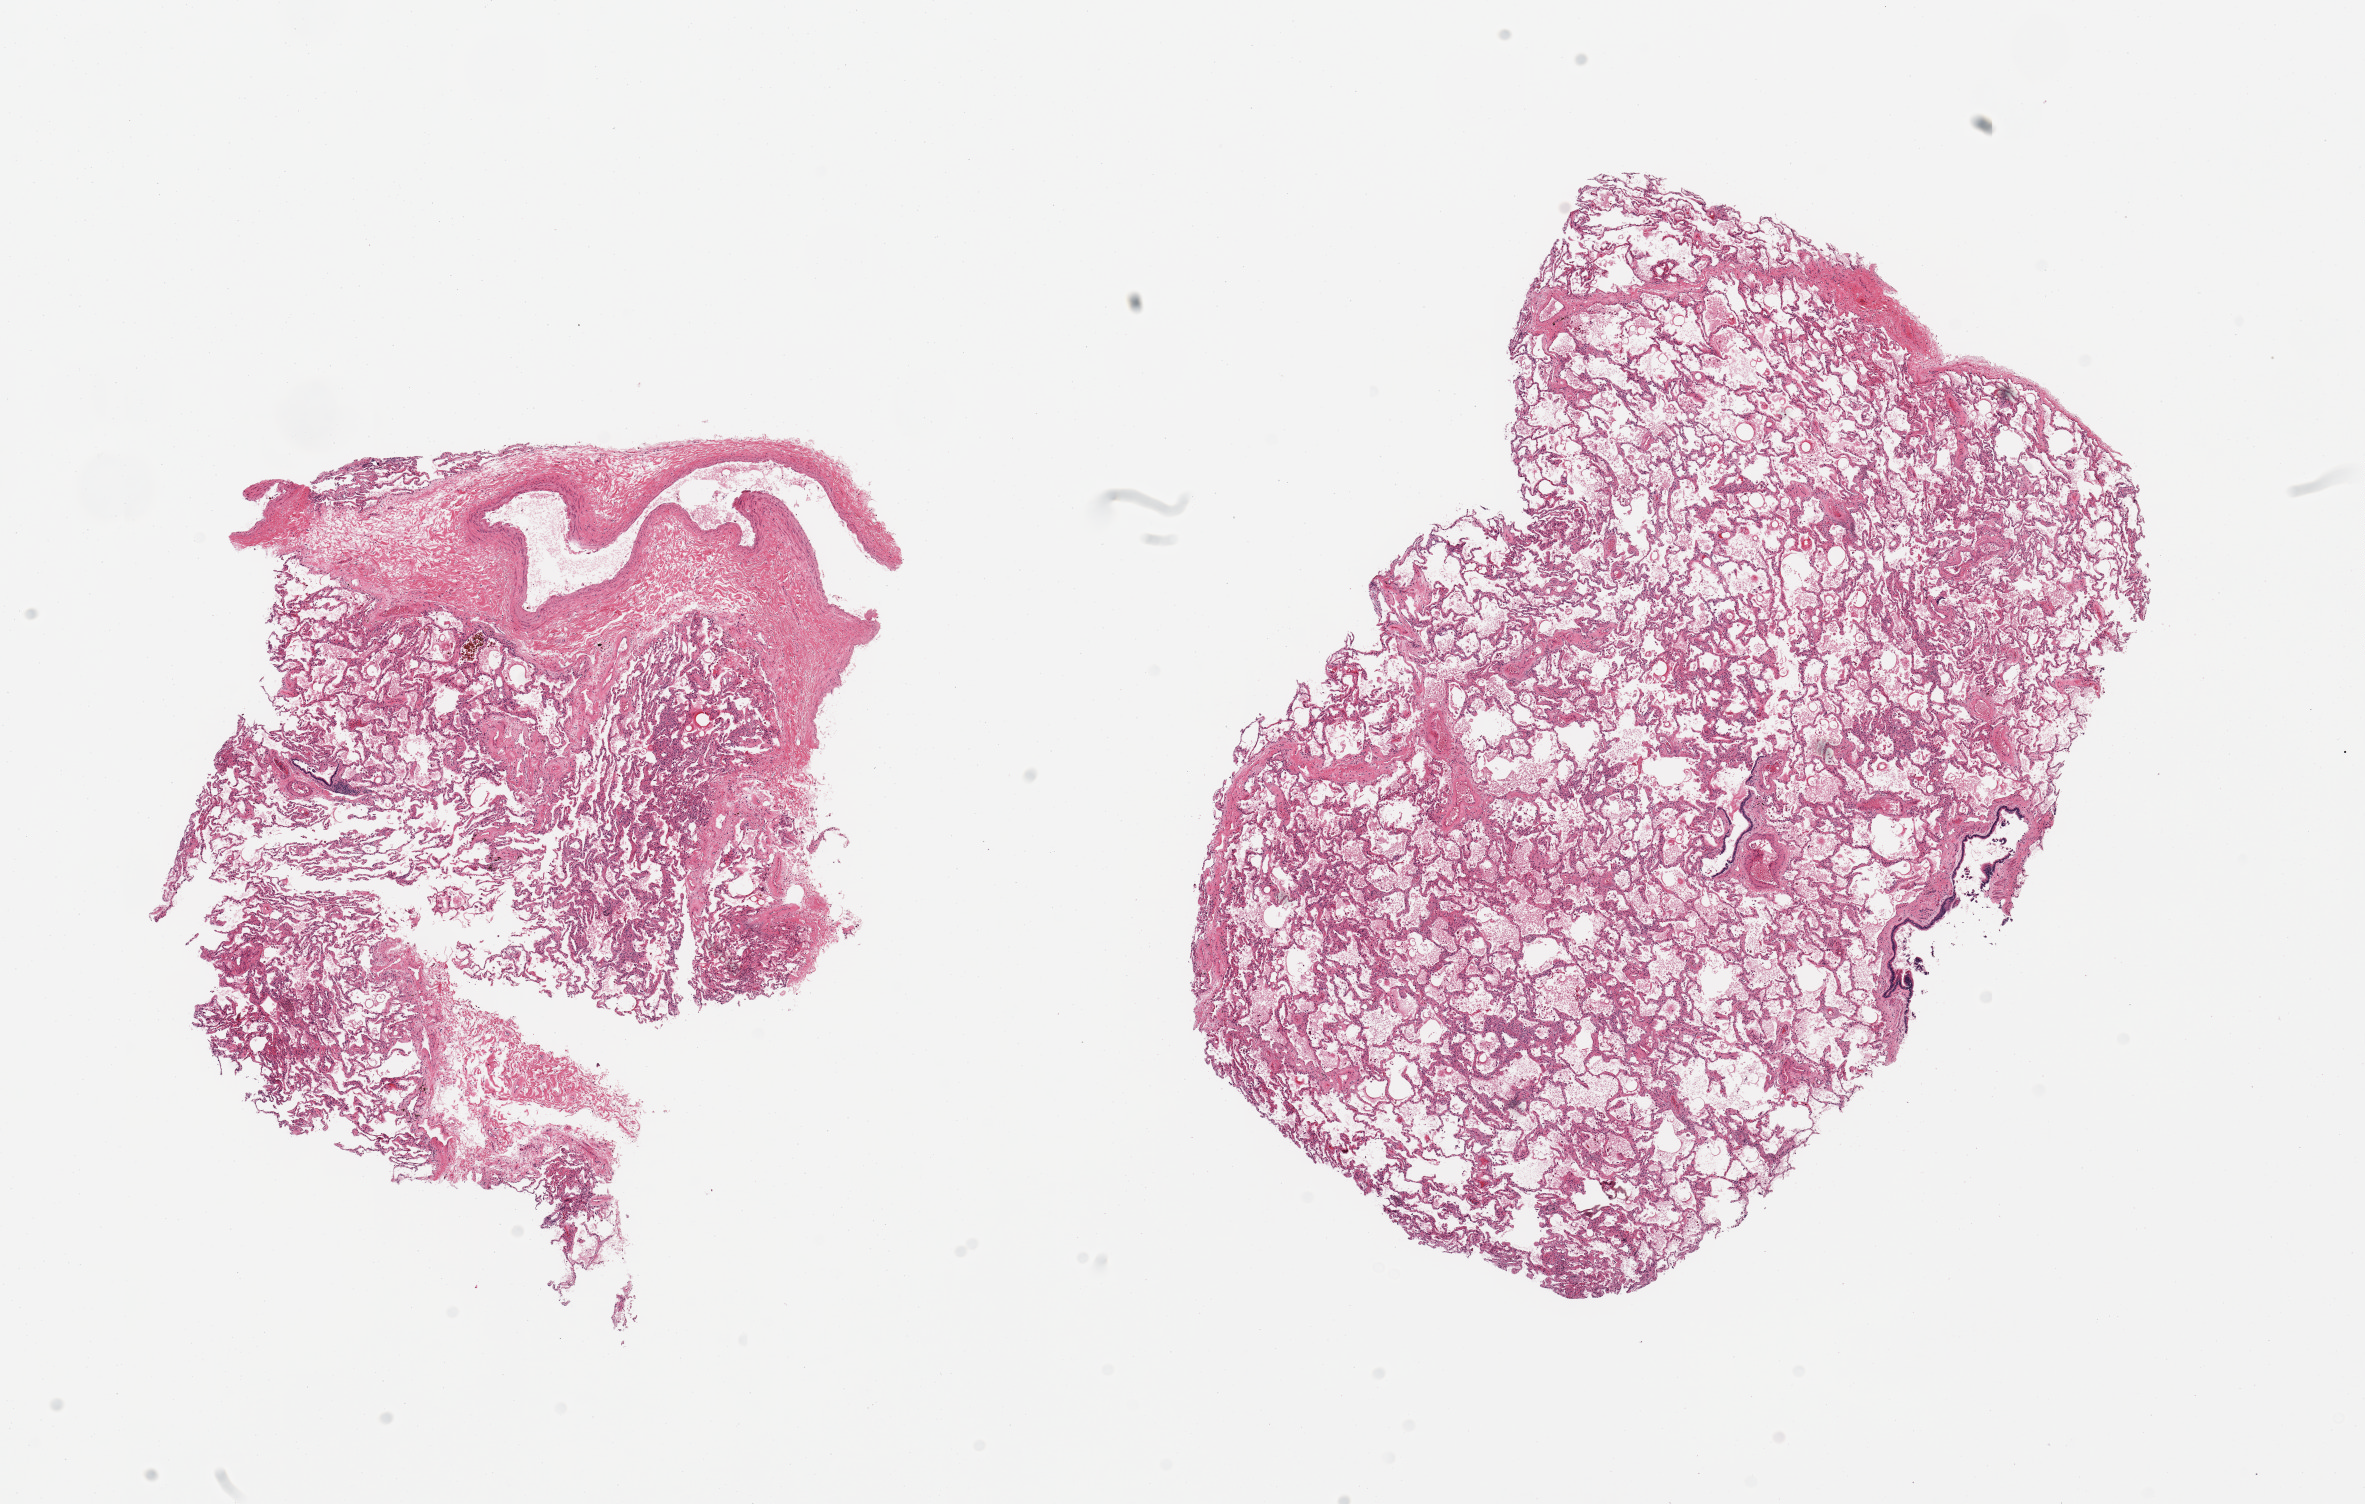
Haematoxylin and eosin whole-slide image — whole scanned area (about 18.7 x 11.9 mm, acquisition: 20x scan) shown as a low-resolution overview, PAXgene-fixed, paraffin-embedded tissue, section of lung (target tissue), donor tissue sample. Donor sex: female.
Reviewer comment on this tissue sample: 2 pieces; one piece contains ~20% of fibrovasular component with large vessels; some thick-walled vessels.